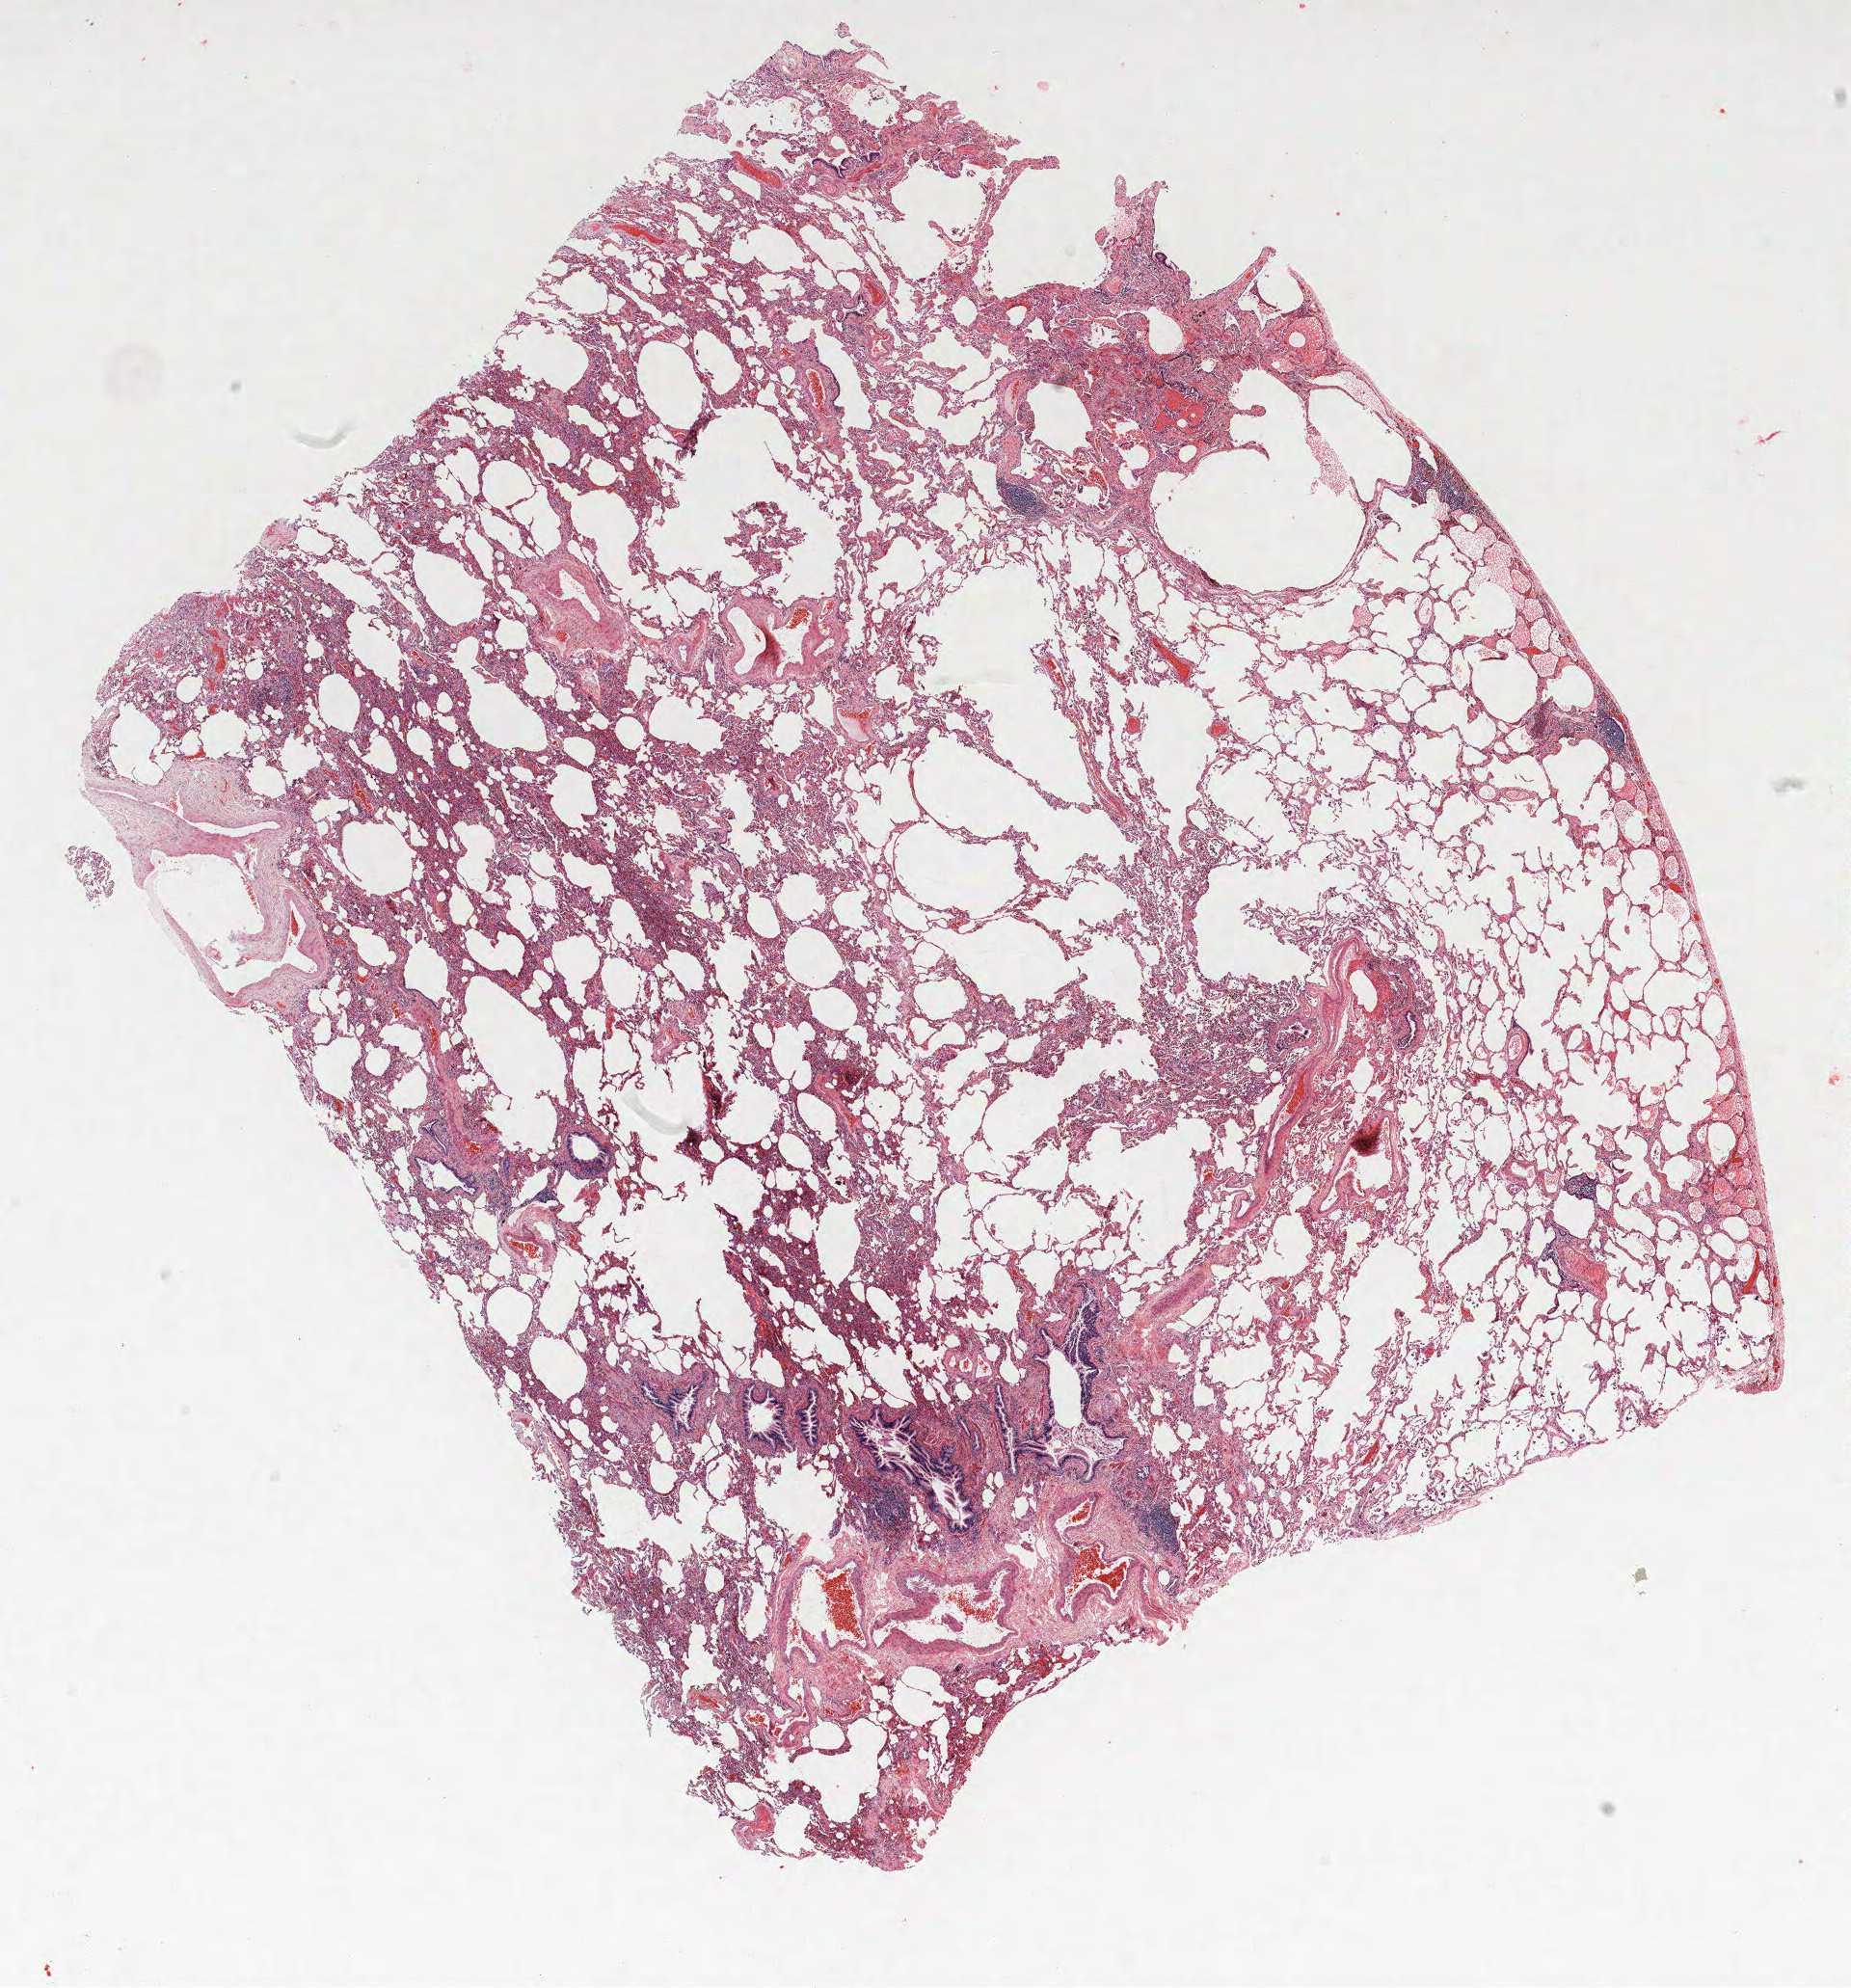
Hematoxylin and eosin (H&E) stained whole-slide image — shown as a low-resolution overview of the whole scanned area (about 15.4 x 16.5 mm, acquisition: 40x scan), formalin-fixed paraffin-embedded (FFPE) section, lung tissue. Female patient, aged 61 at enrolment. Grade: poorly differentiated (G3).
- tumour size (pathology): 17 mm
- participant's lung-cancer diagnosis: Adenocarcinoma, NOS
- primary tumour location (clinical record): left upper lobe
- stage (AJCC 6th edition): IB